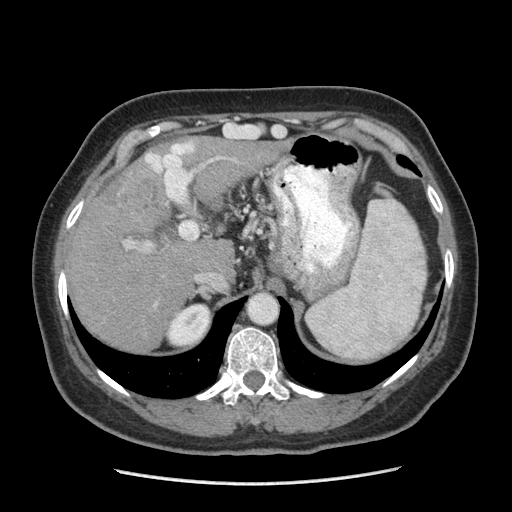
Contrast-enhanced abdominal CT (liver protocol), one axial slice; slice 158 of 185 in the series (ordered by position); reconstruction kernel STANDARD; 140 kVp; soft-tissue window (W 400 / L 40 HU); 512 × 512 image matrix, field of view 360 × 360 mm. Case-level facts recorded for this patient, not image findings: diagnosis: hepatocellular carcinoma (patient treated with transarterial chemoembolisation; whether this scan precedes or follows treatment is not stated here); TNM stage (as recorded): Stage-I; Child-Pugh class: A; tumour differentiation: poorly differentiated.
Outlined on this slice (semi-automatic segmentation, software-assisted and operator-edited):
- abdominal aorta: bounding box <250,295,276,322> (left, top, right, bottom; pixels)
- liver parenchyma outside the tumour (the mass and vessels are separate outlines, so this box may not span the whole liver): <66,136,279,350>
- mass: <114,163,168,228>
- liver vessels: <126,142,223,280>